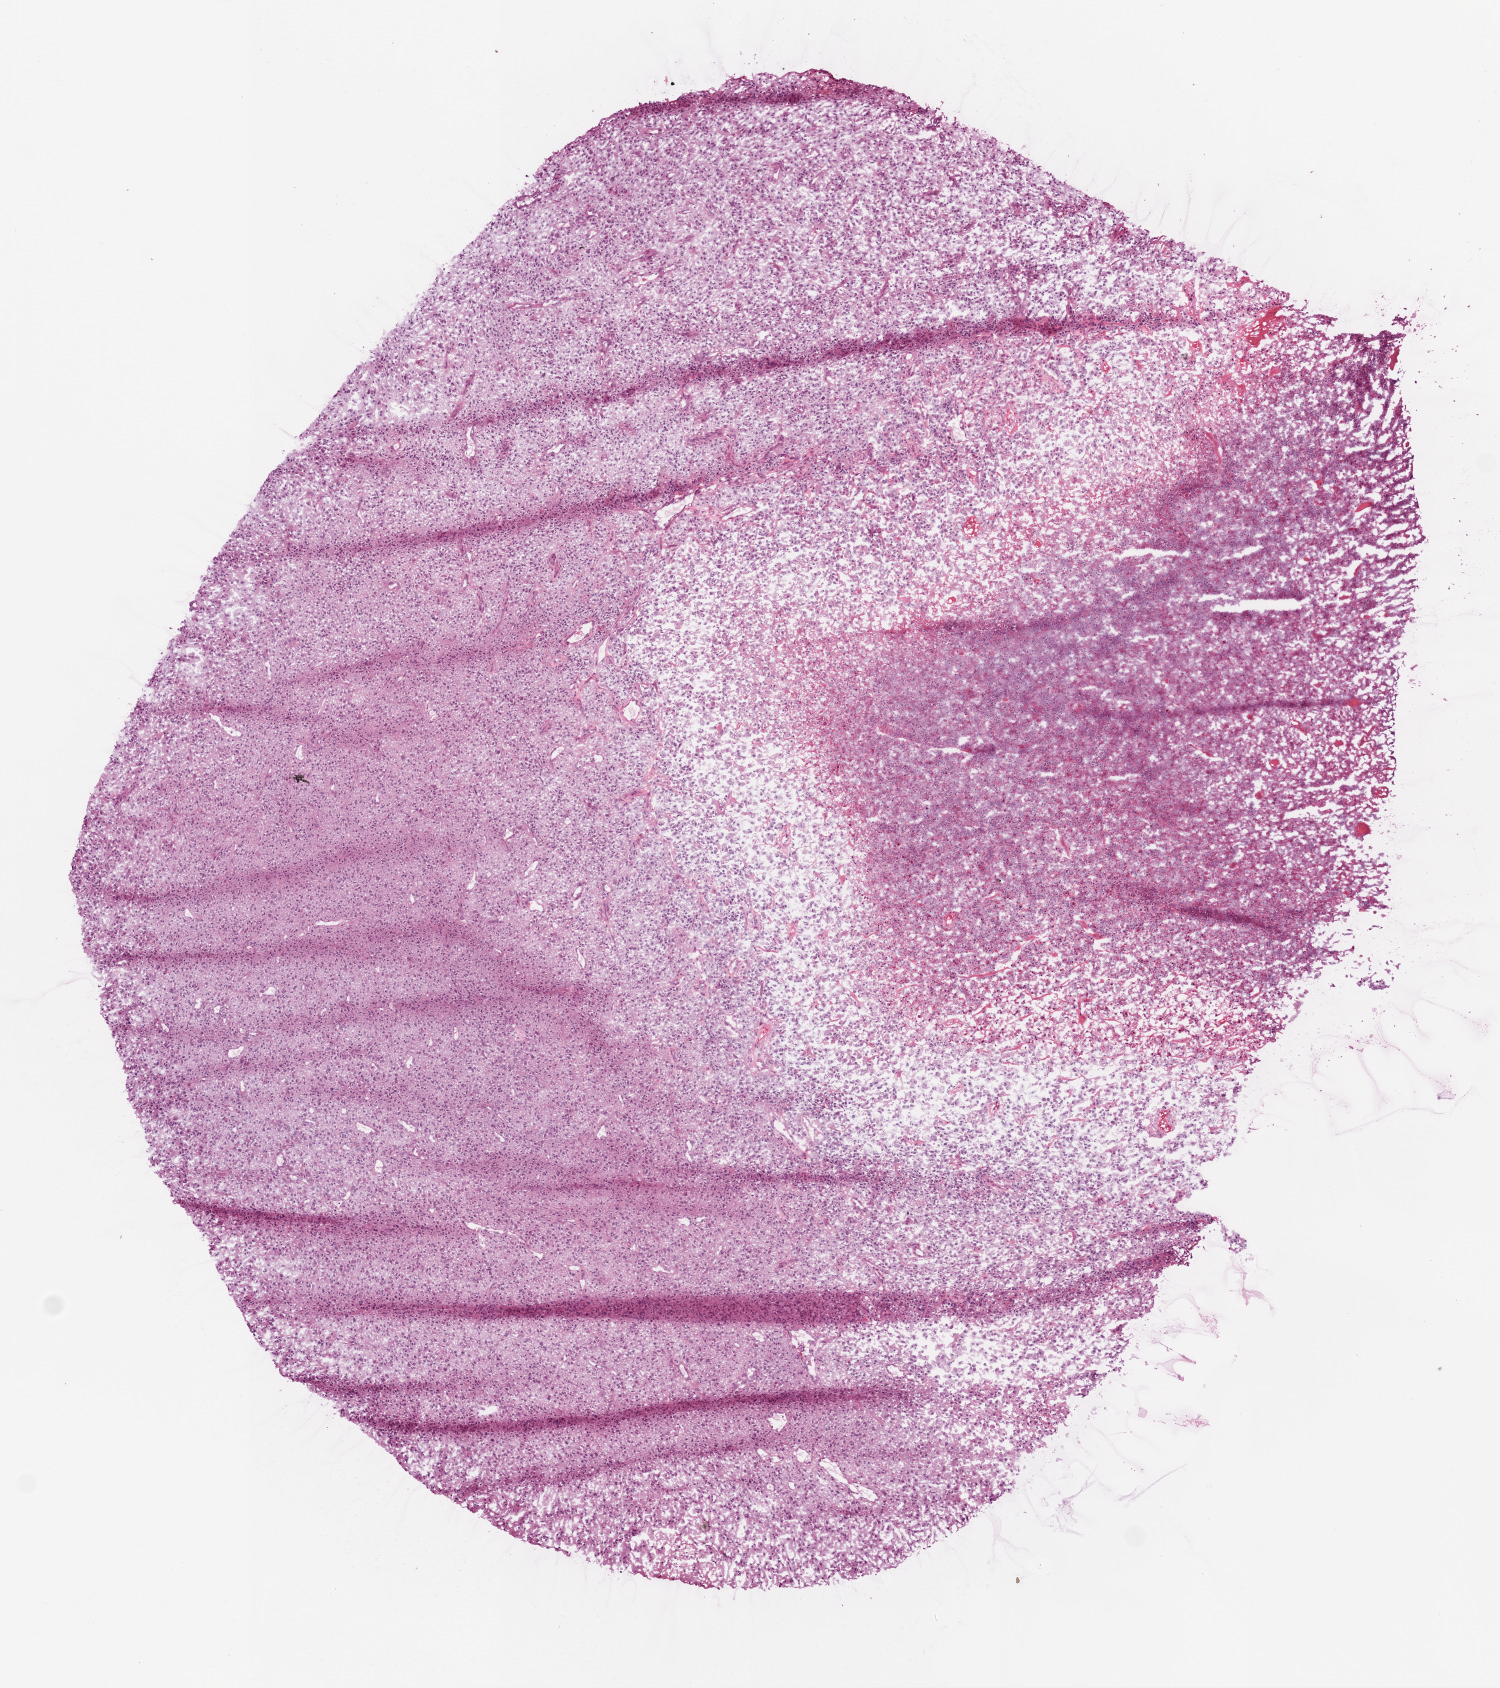
Digitized Hematoxylin and eosin (H&E) stained tissue section (whole slide) — shown as a low-resolution overview of the whole scanned area (about 6.0 x 6.8 mm, slide scanned at 20x), frozen section from the bottom of the tissue portion, brain, primary tumour sample. Female, age 69 years at initial diagnosis.
Pathologic diagnosis: Glioblastoma.